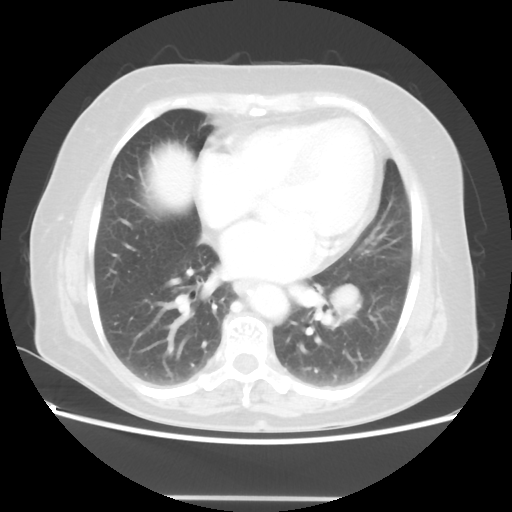
Chest CT, one axial slice. Position 25 of 56 along the scan axis. Reconstruction kernel STANDARD. Lung window (W 1500 / L -600 HU). 512 × 512 image matrix, field of view 360 × 360 mm. Patient: female, 73 years. From the clinical record (not read from this slice): clinical TNM (as recorded): T1c N0 M0.
Annotated regions visible in this slice (rectangle marked by the reading radiologist):
- lung tumour (recorded histology: adenocarcinoma): bounding box (x1, y1, x2, y2) in pixels: (327, 277, 366, 321)